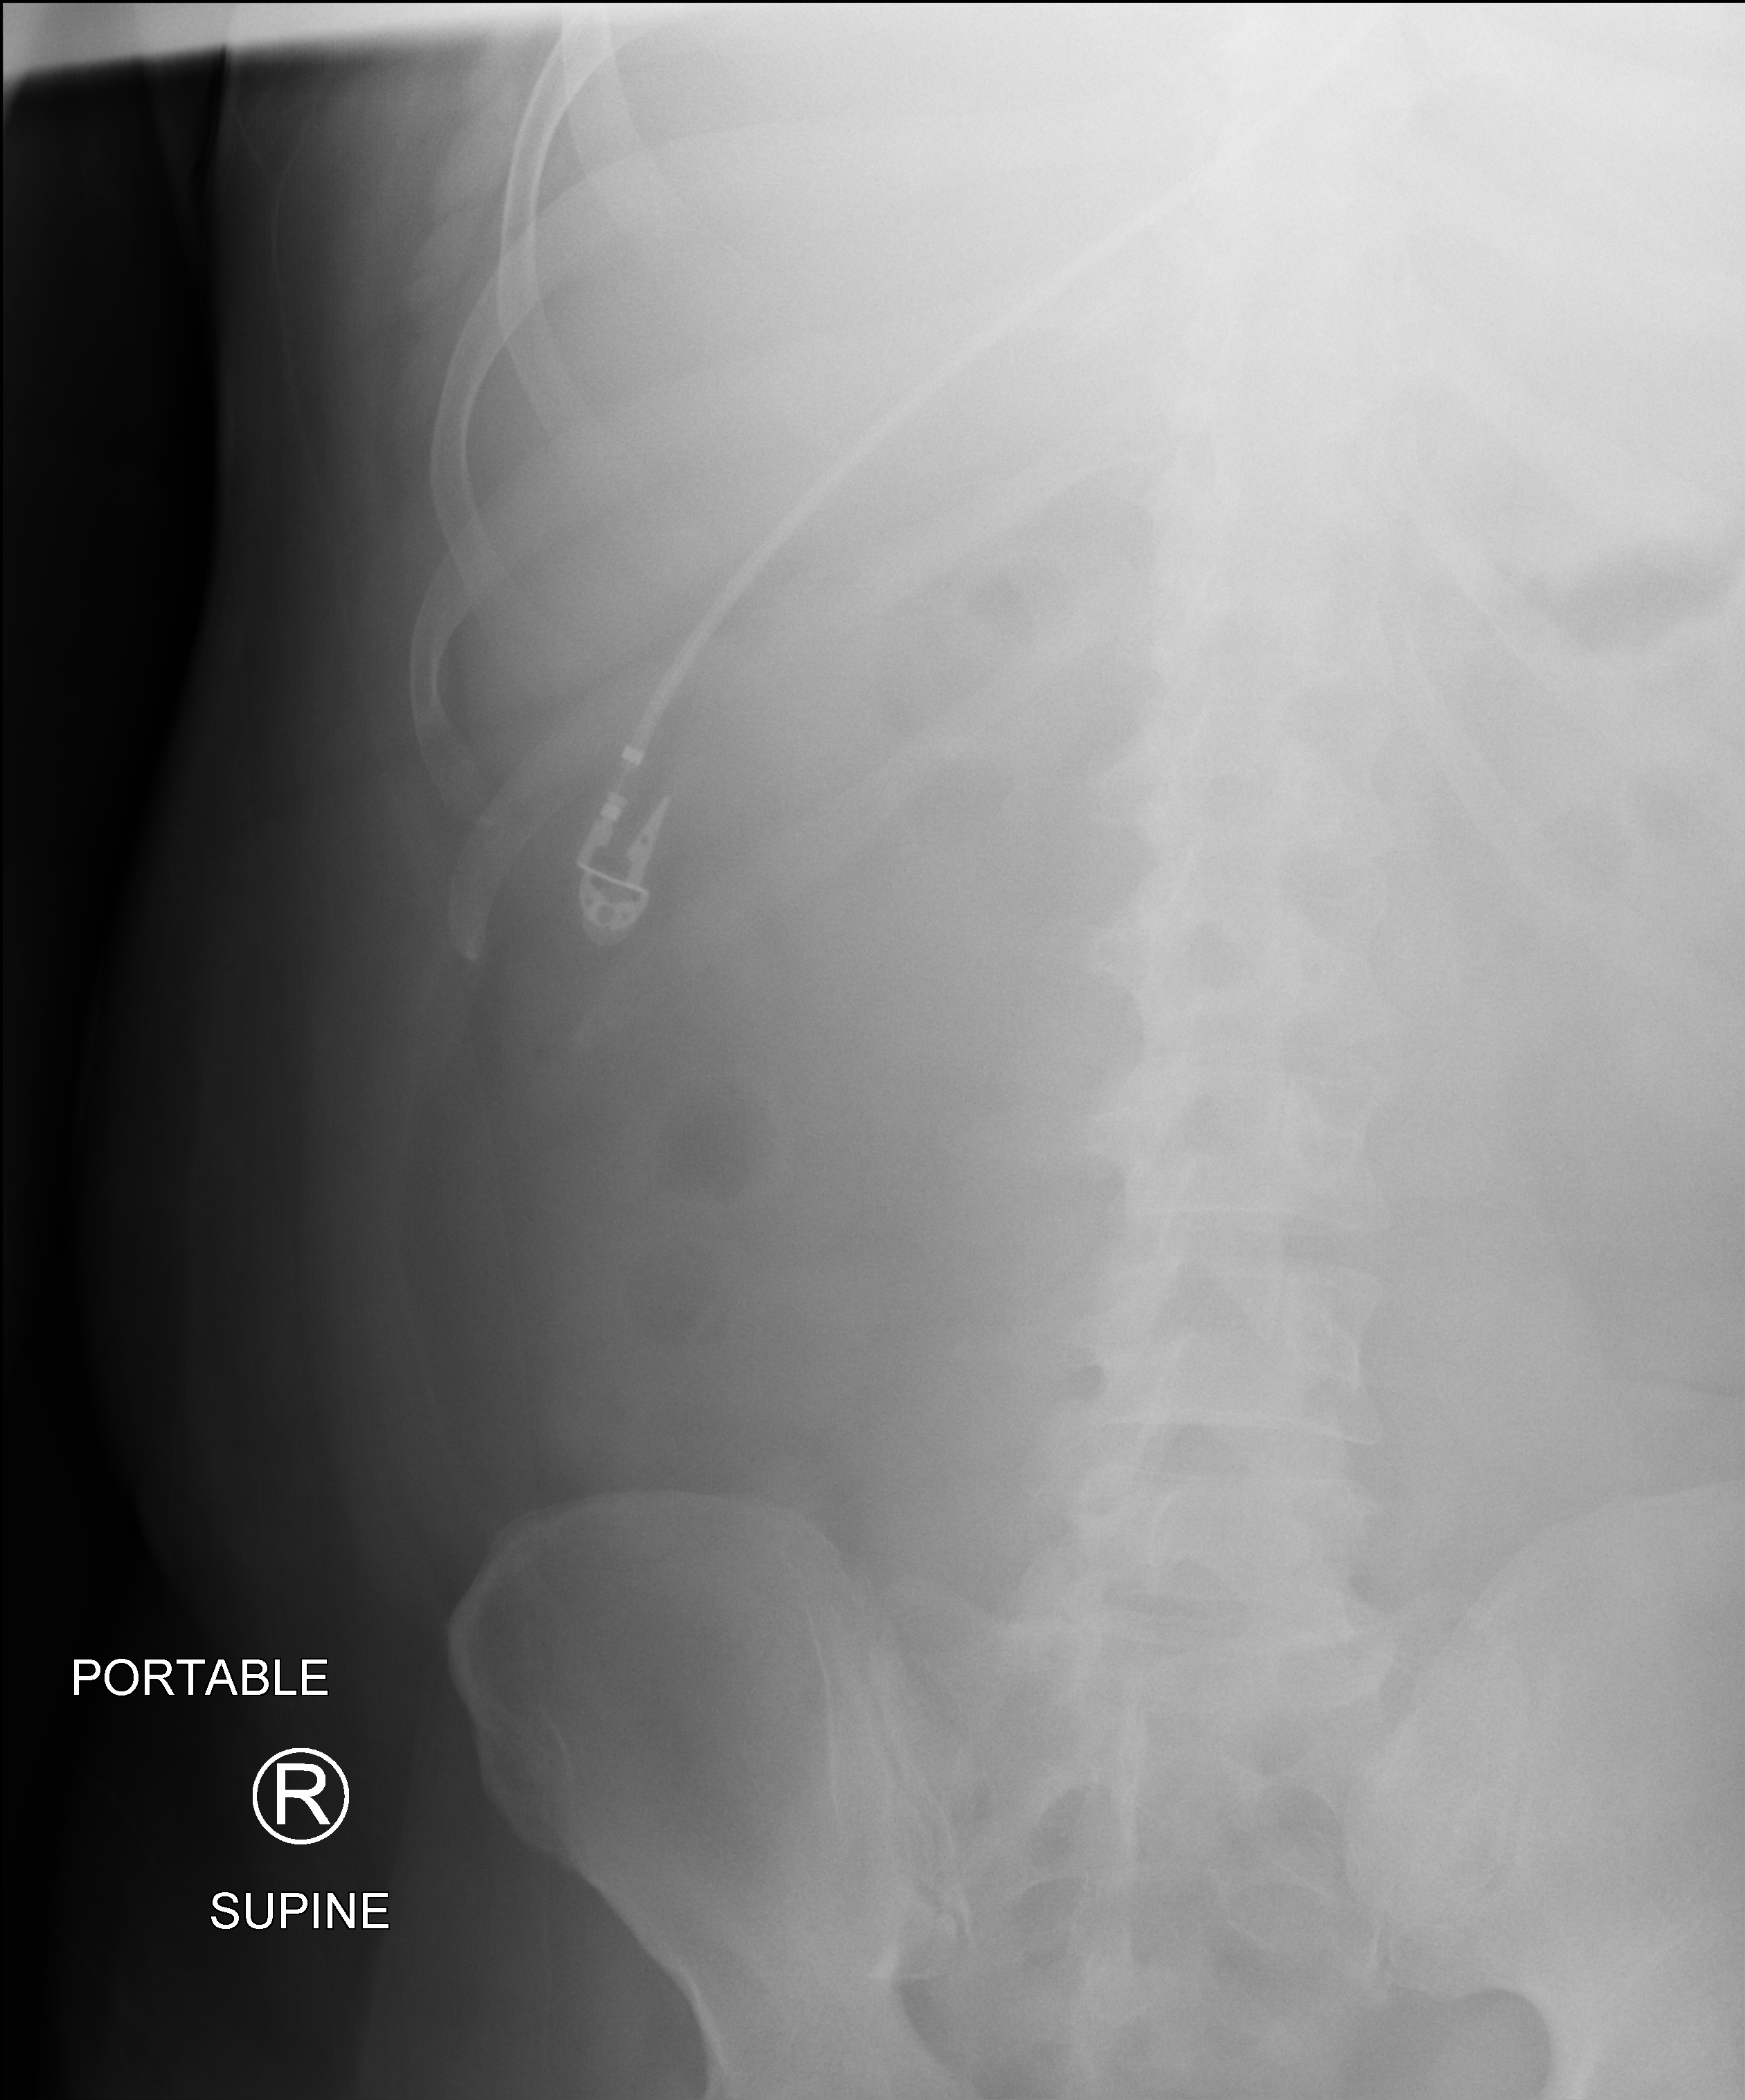
Portable abdomen radiograph, anteroposterior (AP) projection. Male patient hospitalised with COVID-19, age 18–59 years.
Hospital-stay facts (about this admission, not read from this image; timing relative to this image not recorded): admitted to intensive care during this hospital stay: yes.